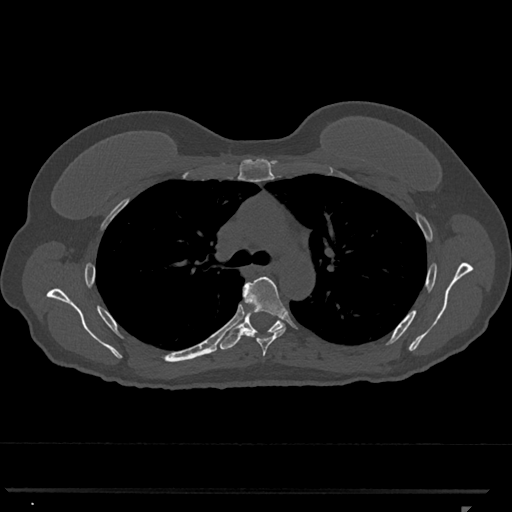
CT including the spine, one axial slice; slice 788 of 793 in the series (ordered by position); reconstruction kernel Br40s/3; bone window (W 1800 / L 400 HU); 512 × 512 image matrix. Female patient, age 62 years. From the clinical record (not read from this slice): primary cancer: renal.
Outlined on this slice (semi-automatic segmentation, software-assisted and operator-edited):
- T5 vertebra: bounding box <240,277,288,357> (left, top, right, bottom; pixels)
- T6 vertebra: <219,286,283,350>